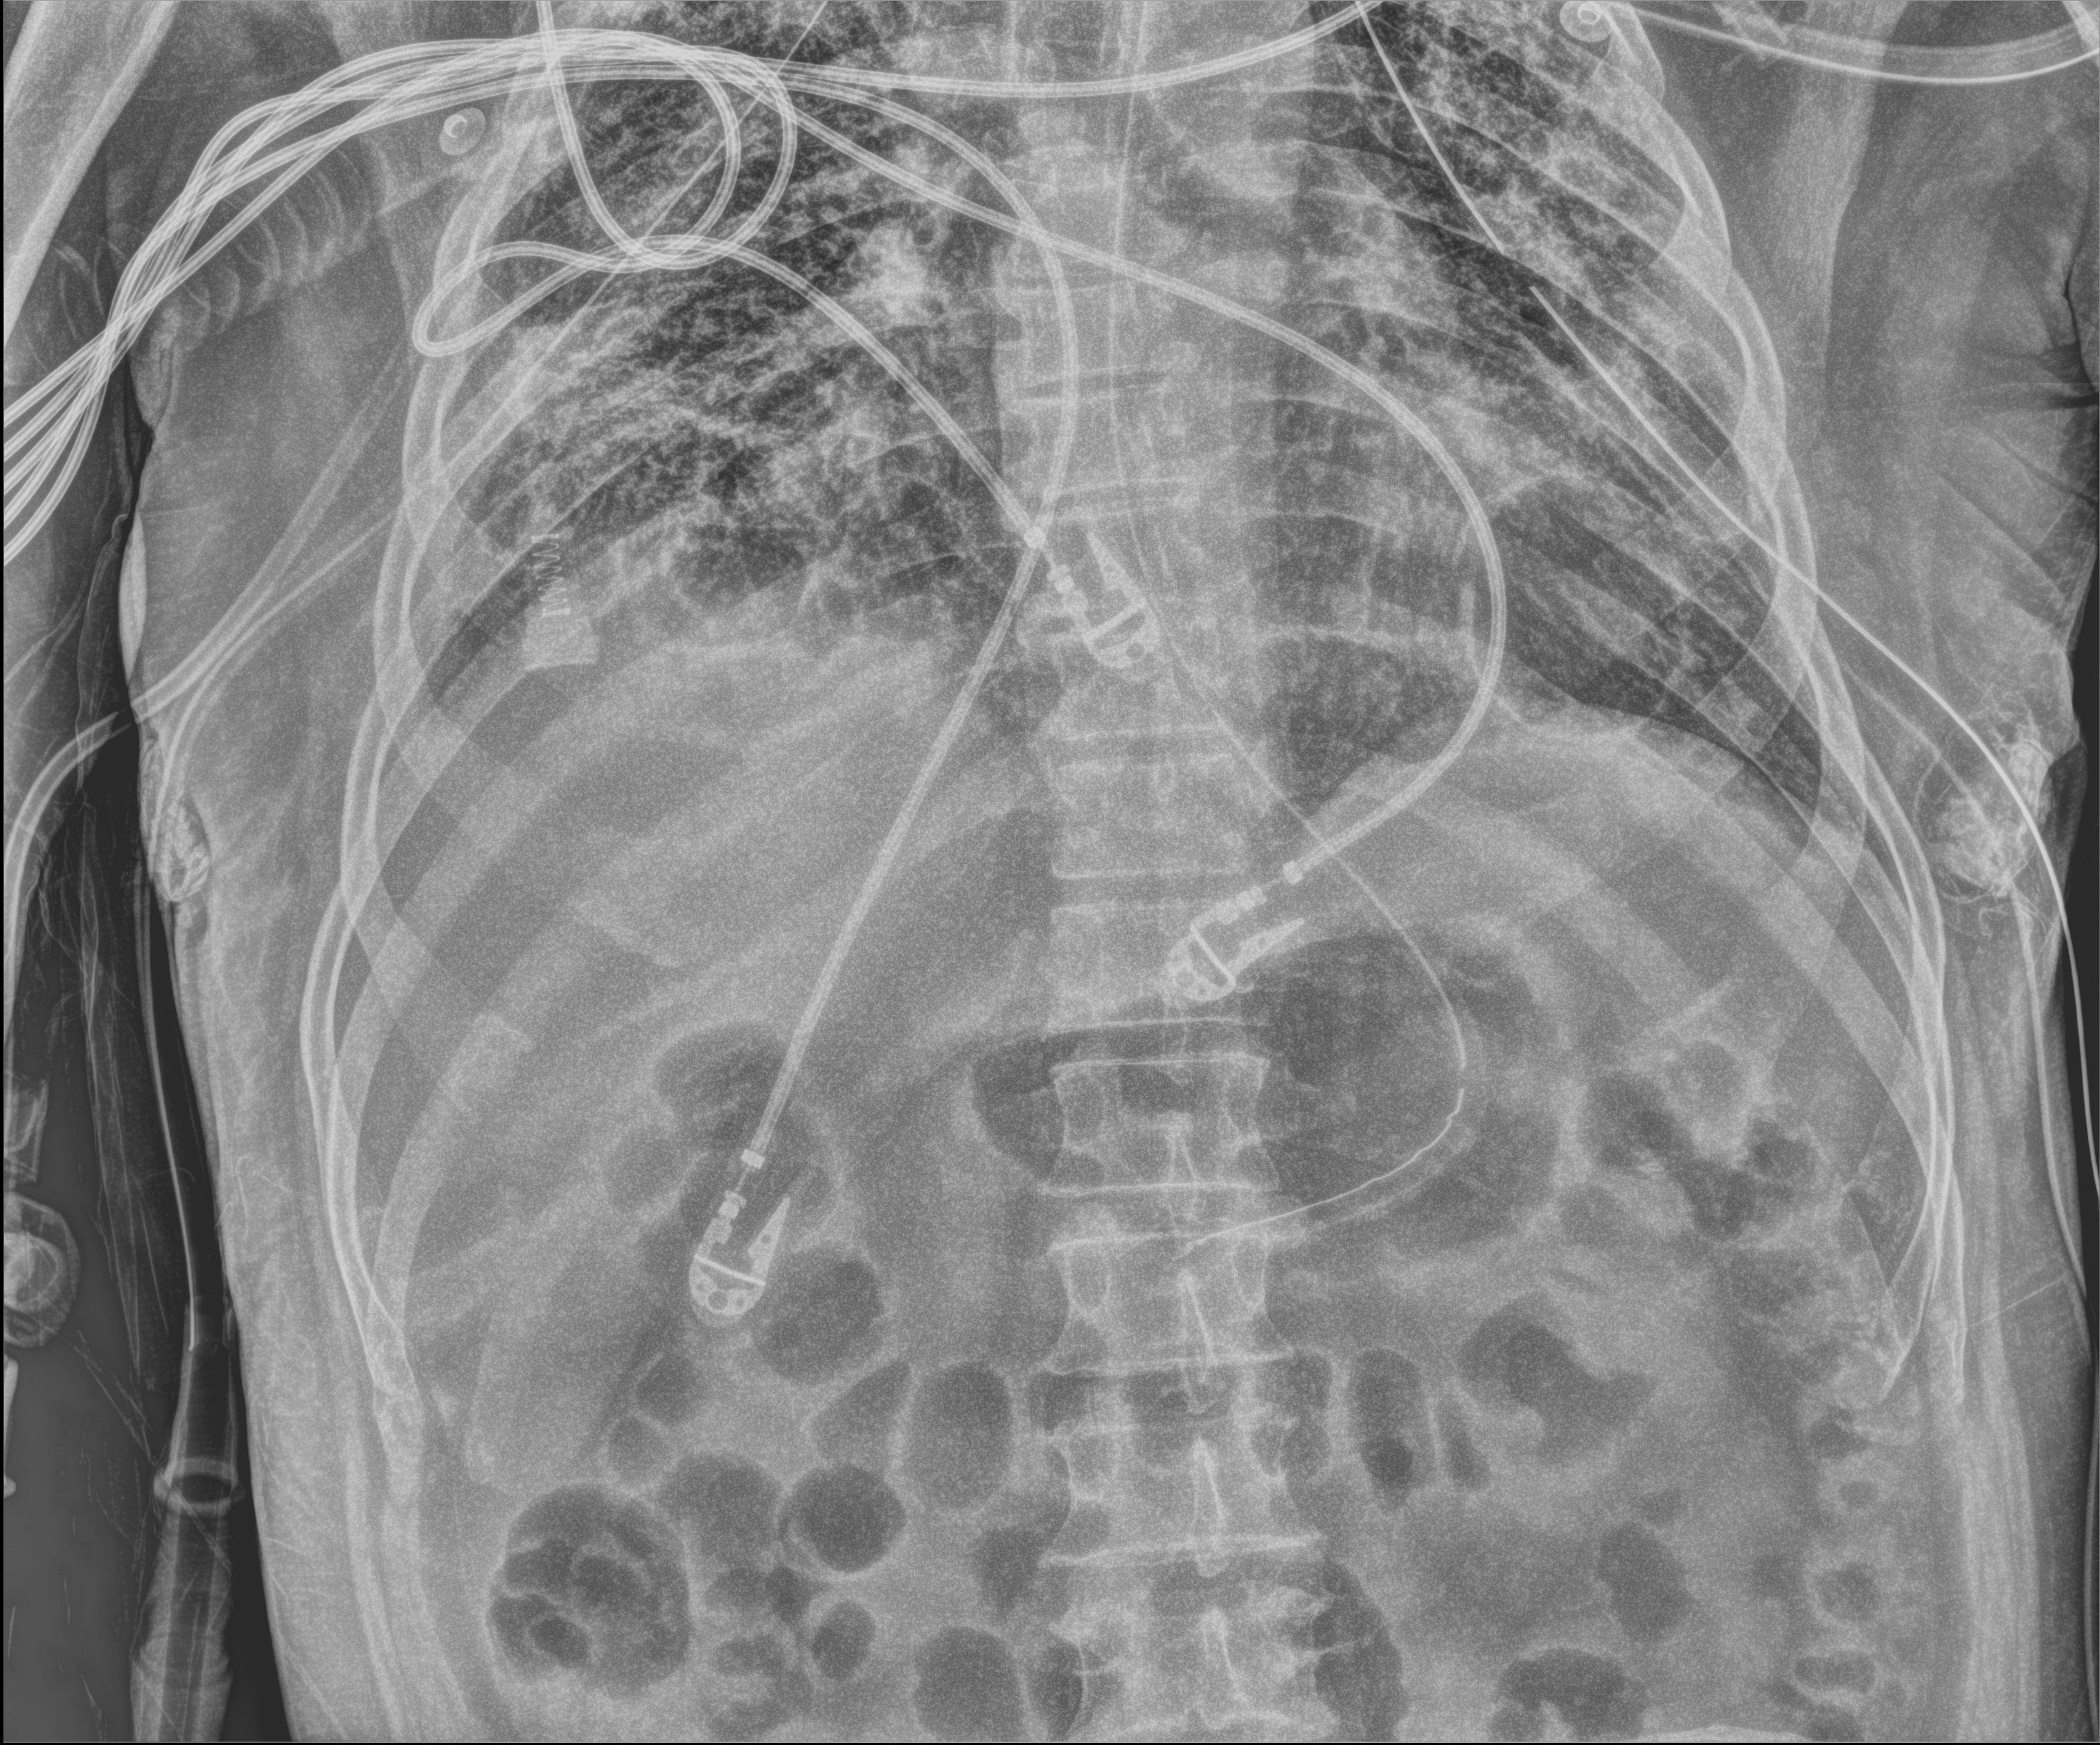
Chest X-ray (portable); anteroposterior (AP) projection. Male patient hospitalised with COVID-19, age 18–59 years.
From the hospital-stay record, not from the radiograph (when in the stay this image was taken is not recorded):
- smoking status (admission record): never